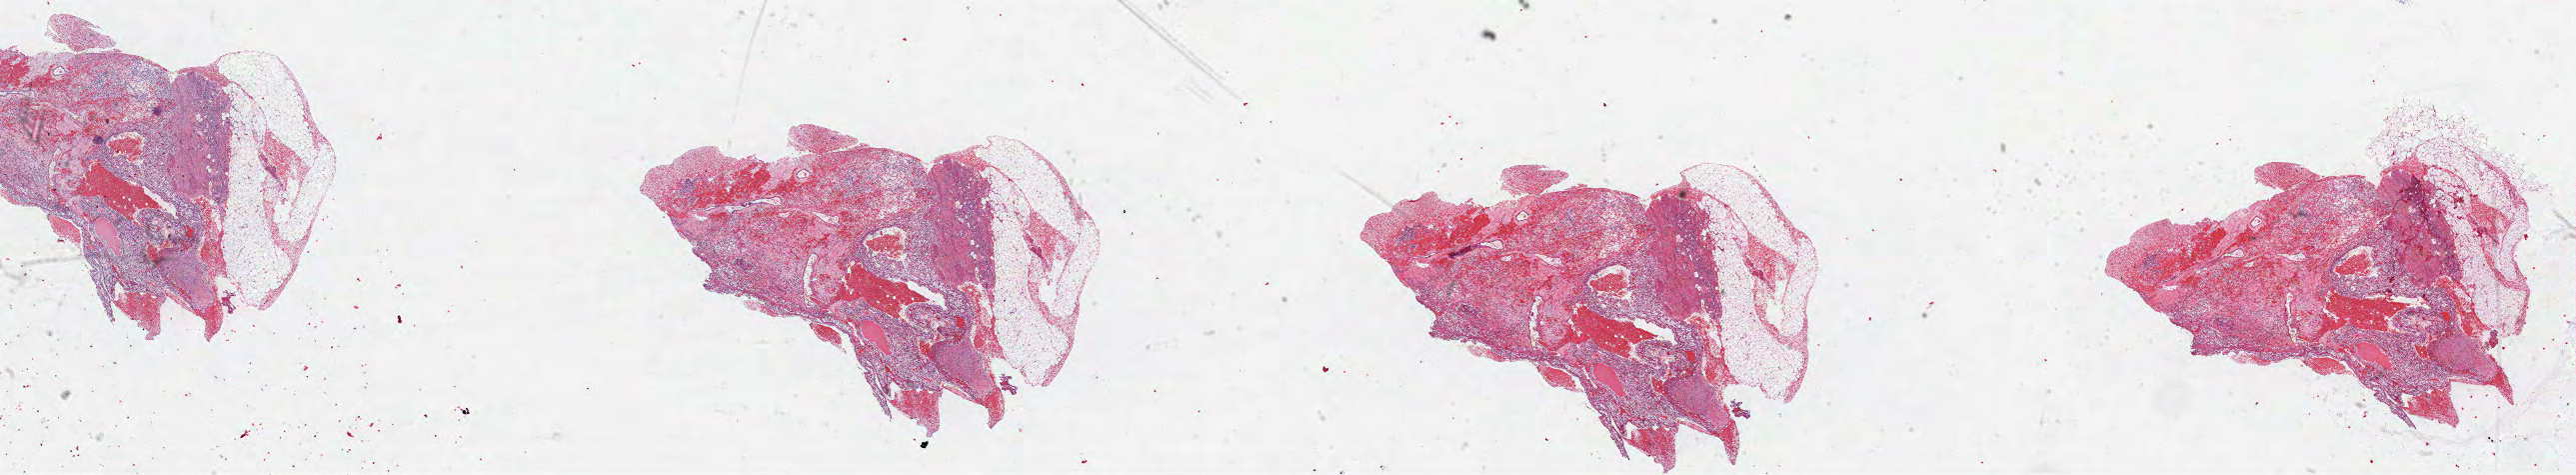
Digitized H&E-stained tissue section (whole slide), a low-resolution overview of the entire scanned area, about 41.6 x 7.7 mm; FFPE section; sample: primary tumour, kidney. Male patient; age at initial diagnosis 83 years. Histologic grade: G3 (poorly differentiated).
Diagnosis: Clear cell adenocarcinoma, NOS. Laterality: right. AJCC pathologic stage: I (7th edition).